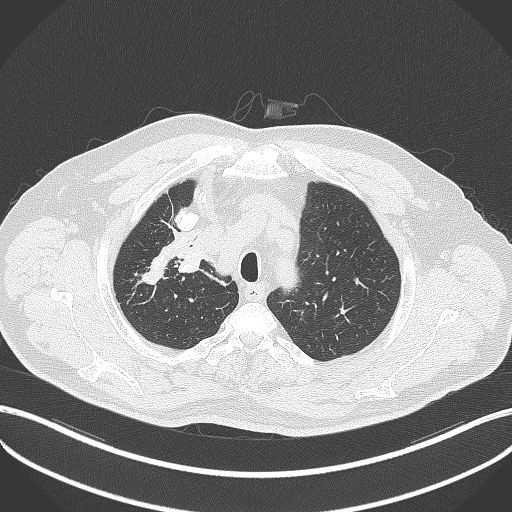
Chest CT, one axial slice; slice 318 of 411 in the series (ordered by position); reconstruction kernel B70f; 120 kVp; lung window (W 1500 / L -600 HU); 1 mm slice thickness; 512 × 512 image matrix. Patient: male, 60 years. From the clinical record (not read from this slice): clinical TNM (as recorded): T1b N1 M0.
Structures marked on this image (rectangle marked by the reading radiologist):
- lung tumour (recorded histology: squamous cell carcinoma): box from (x=171, y=229) to (x=208, y=275) px